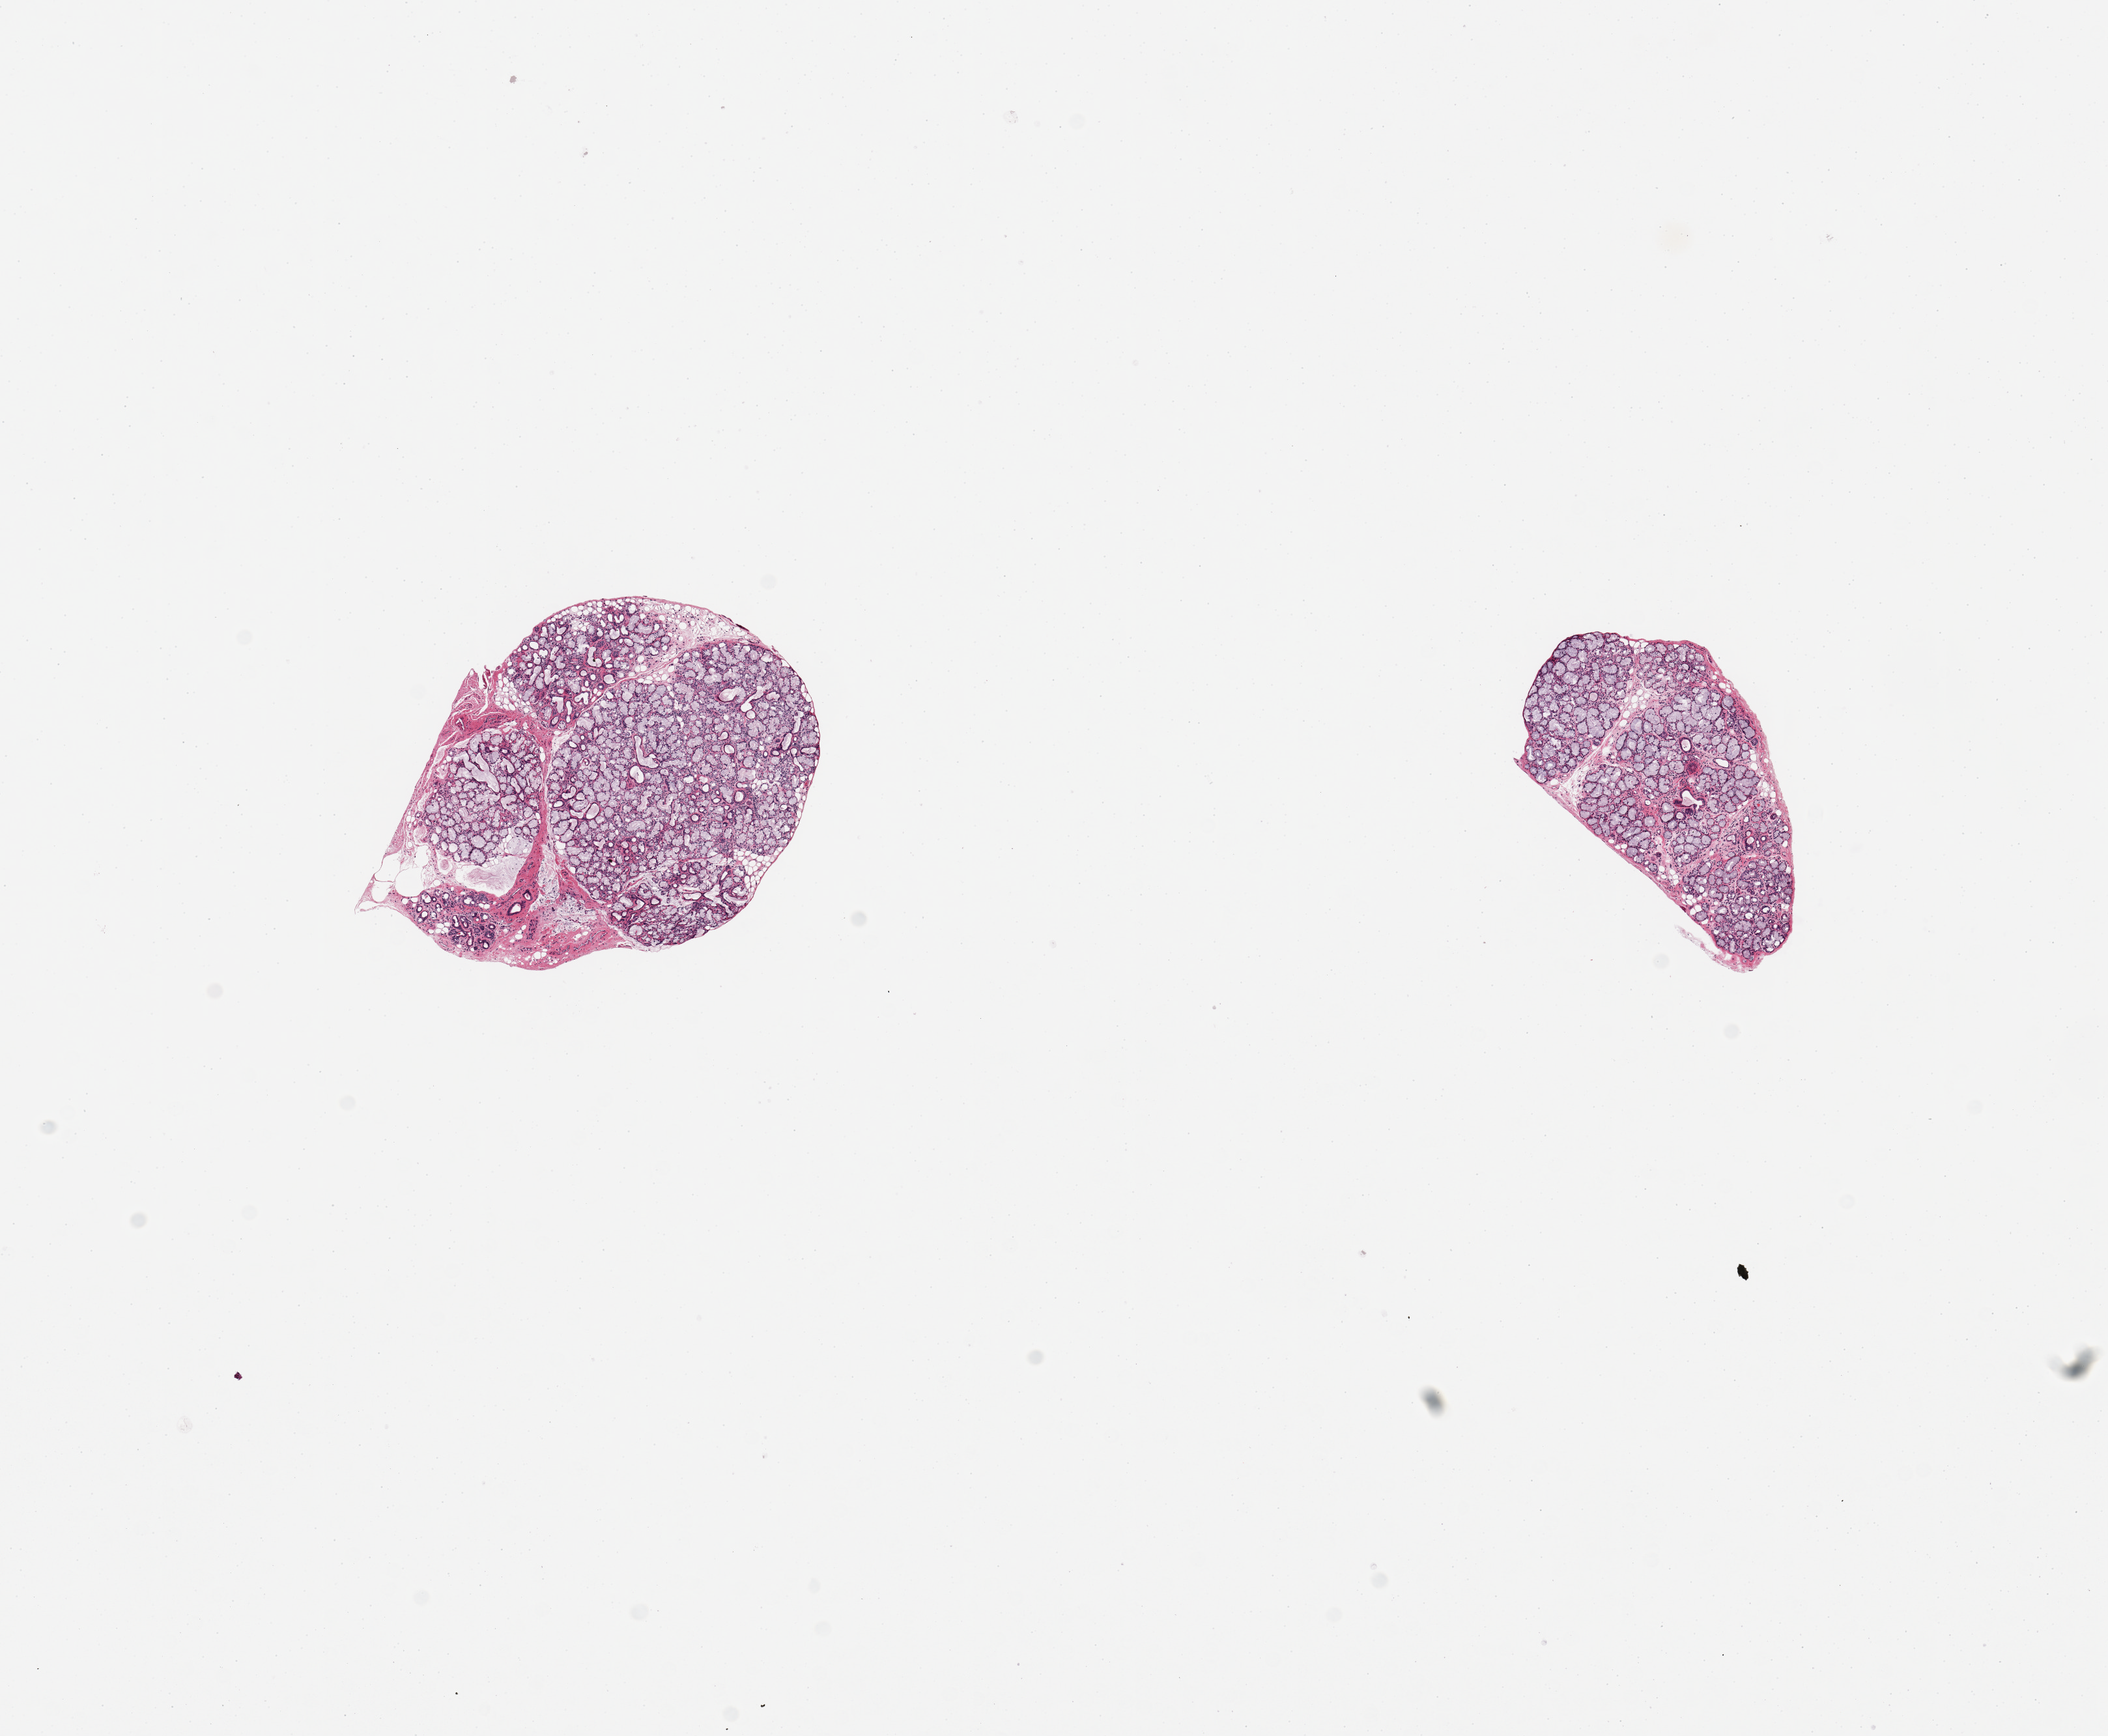
Hematoxylin and eosin (H&E) whole-slide image, brightfield — low-resolution overview of the scanned area, about 12.8 x 10.5 mm (from a 20x scan); PAXgene-fixed paraffin-embedded (PFPE) section; target tissue: minor salivary gland; donor tissue sample. Male donor.
* reviewer comment on this tissue sample: 2 pieces; excellent specimen